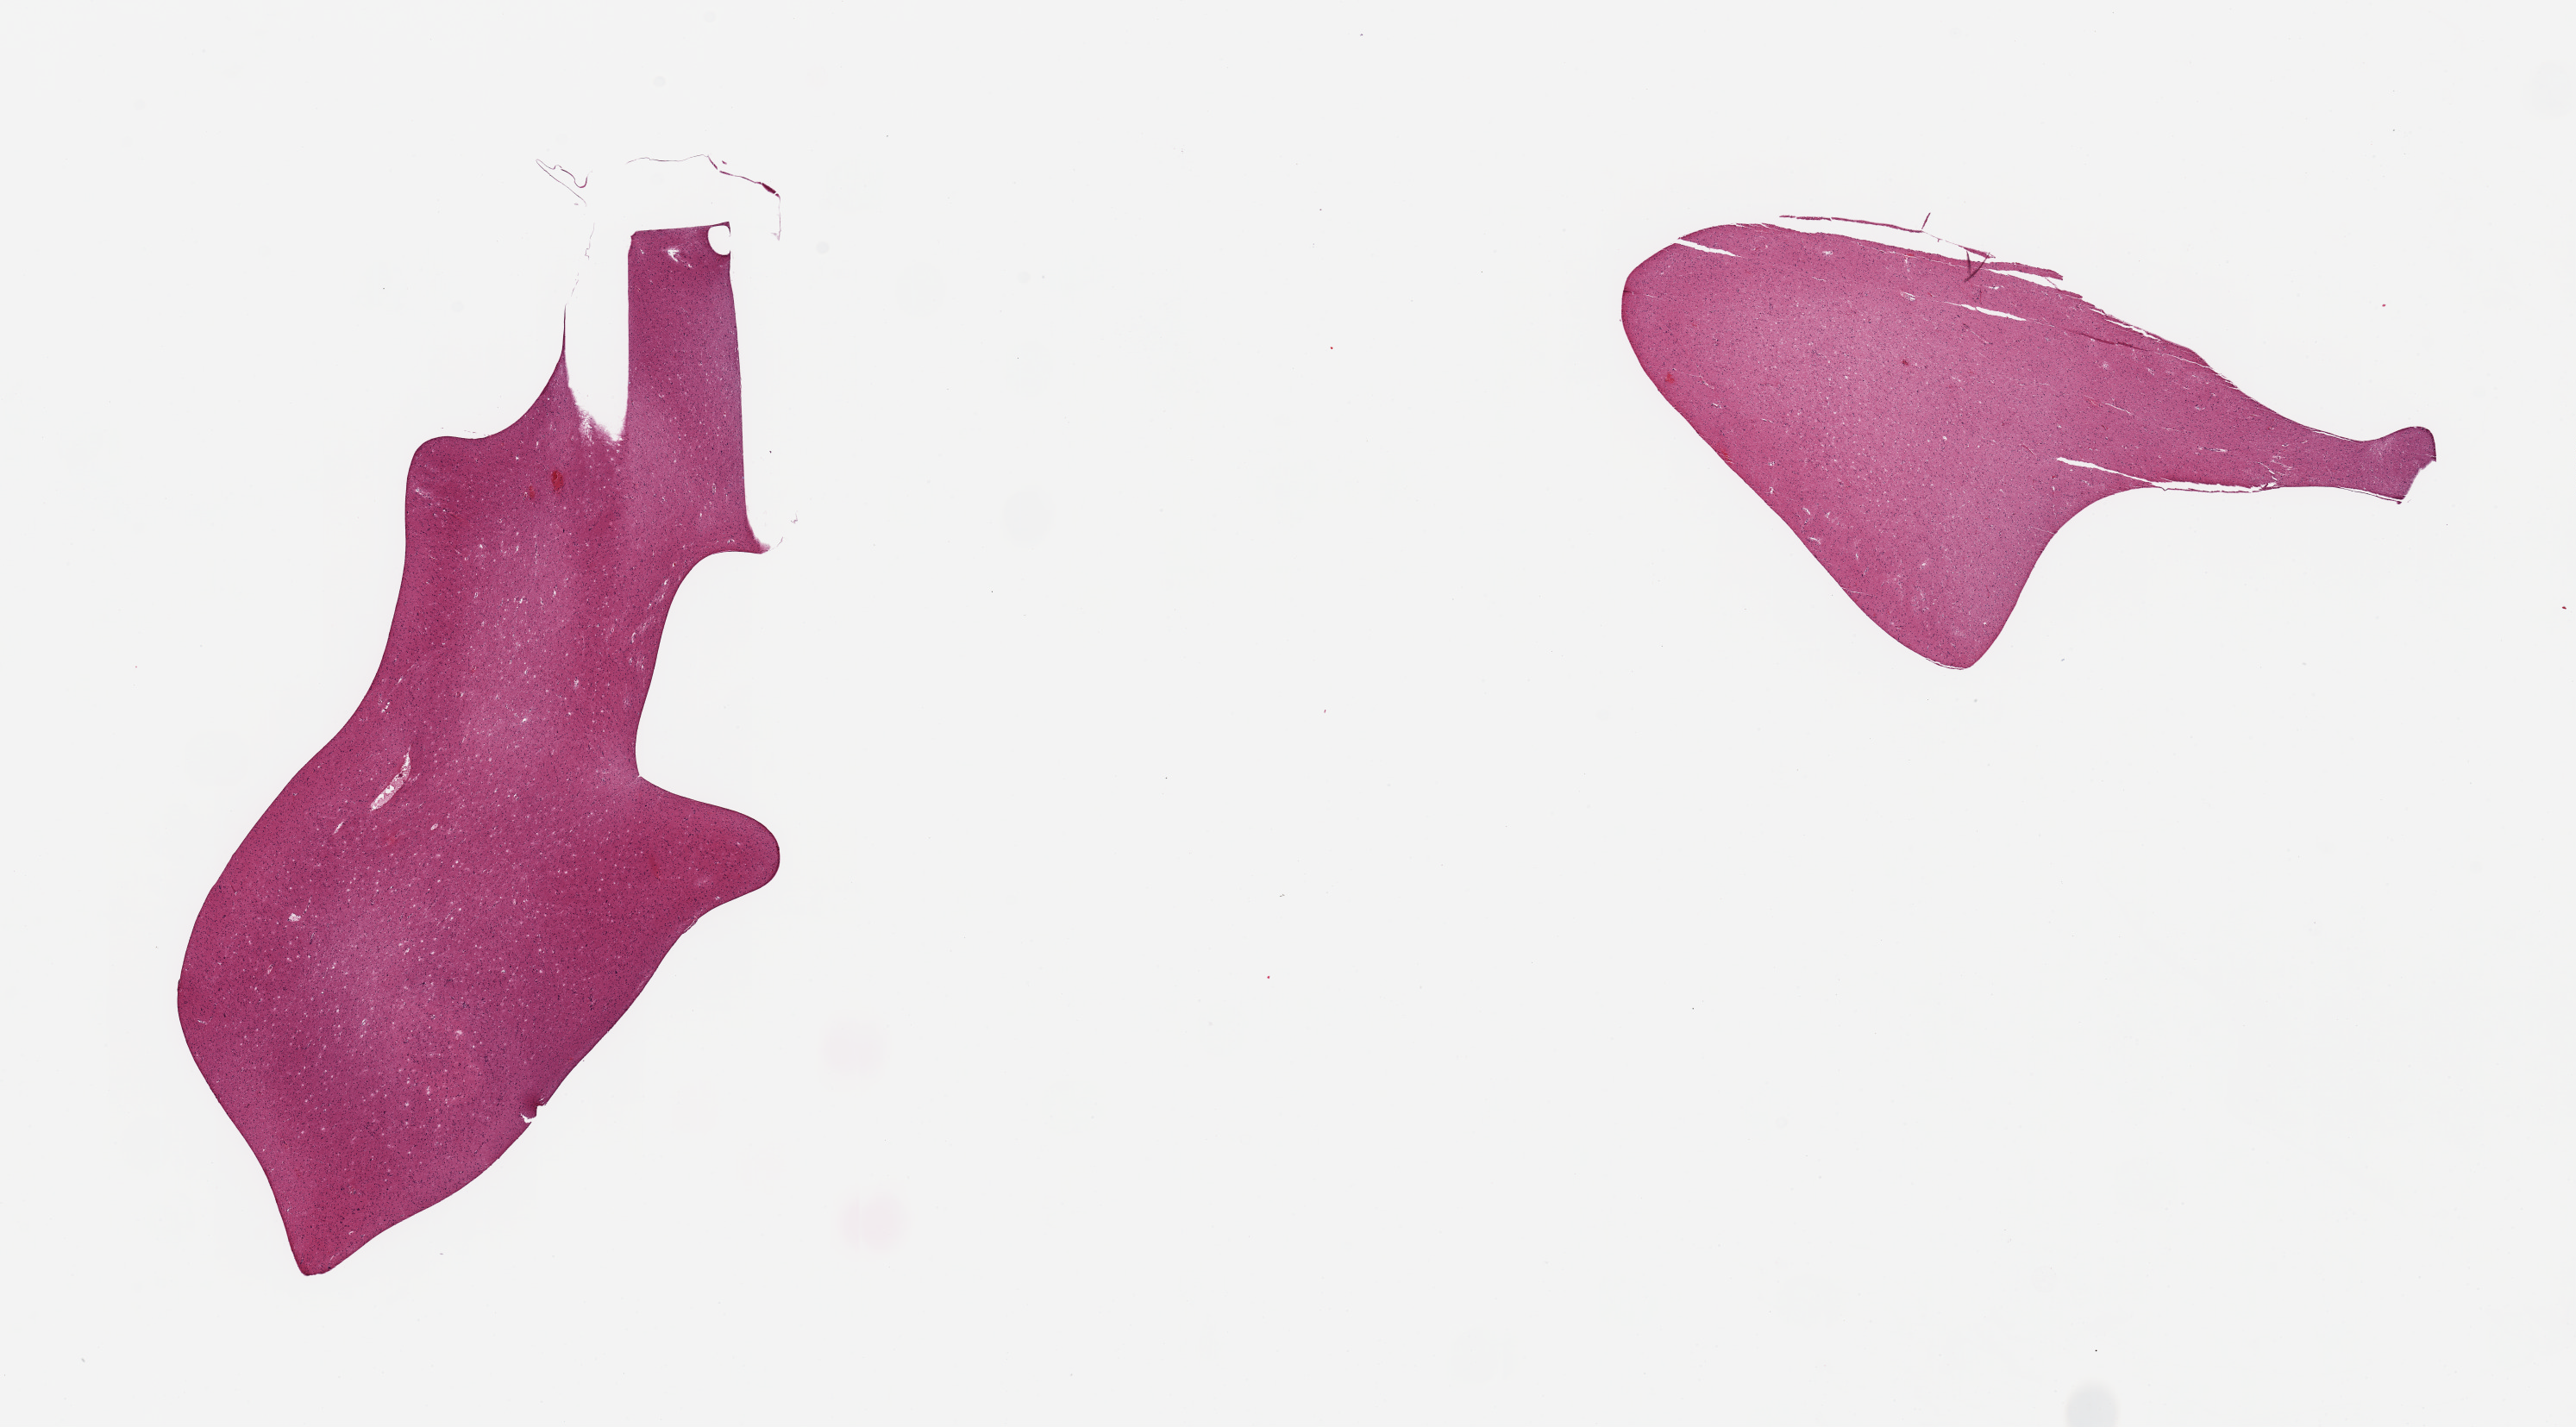
Haematoxylin and eosin whole-slide image, whole scanned area (about 23.6 x 13.1 mm) shown as a low-resolution overview; PAXgene-fixed paraffin-embedded (PFPE) section; section of cerebral cortex (target tissue); donor tissue sample. Donor sex: male.
Review note (as recorded): 2 pieces.